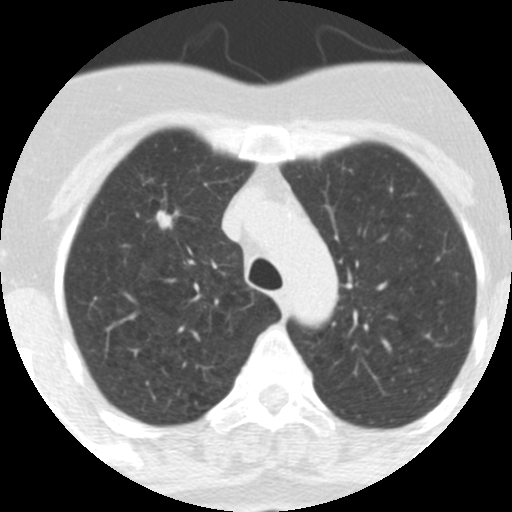
Chest CT (low-dose screening protocol), one axial image; baseline annual screen; lung window (W 1500 / L -600 HU); standard (soft-tissue) reconstruction kernel (STANDARD); 120 kVp; slice 72 of 313 in the series; 512 × 512 image matrix. Female participant, aged 62 years at enrolment.
Lesion marked by an expert reader, bounding box <116,162,184,233> (left, top, right, bottom; pixels). The exam's reader record, not a measurement of the box and not confirmed to be the same lesion: non-calcified nodule or mass ≥4 mm, right upper lobe, 9 × 7 mm, spiculated (stellate) margins, soft tissue attenuation. Participant outcome: lung cancer diagnosed 126 days after this screen — adenocarcinoma, NOS, right upper lobe, moderately differentiated (G2), stage IA (AJCC 6th edition), 18 mm at pathology.